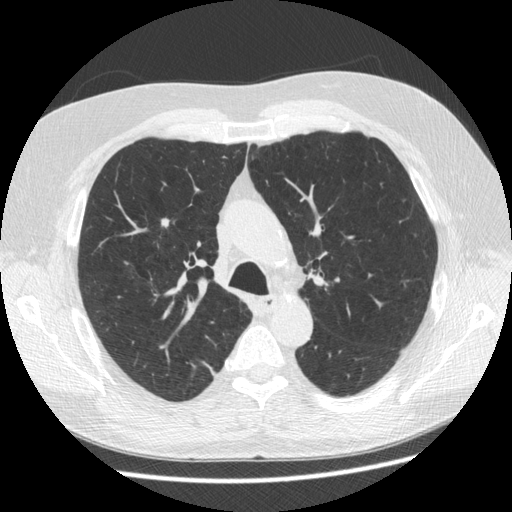
Chest CT (low-dose screening protocol), one axial image. Third annual screen. Lung window (W 1500 / L -600 HU). 1.25 mm slice thickness. Slice 163 of 545 in the series. Male, age 63 years at enrolment. Former smoker at enrolment.
• Expert reader's lesion annotation, box from (x=150, y=209) to (x=183, y=238) px.
• The screening reader recorded 2 non-calcified nodules or masses ≥4 mm on this exam; which of them this box marks is not recorded.
• Participant outcome: lung cancer diagnosed 342 days after this screen — adenocarcinoma, NOS, right upper lobe, stage IIA (AJCC 6th edition), 8 mm at pathology.